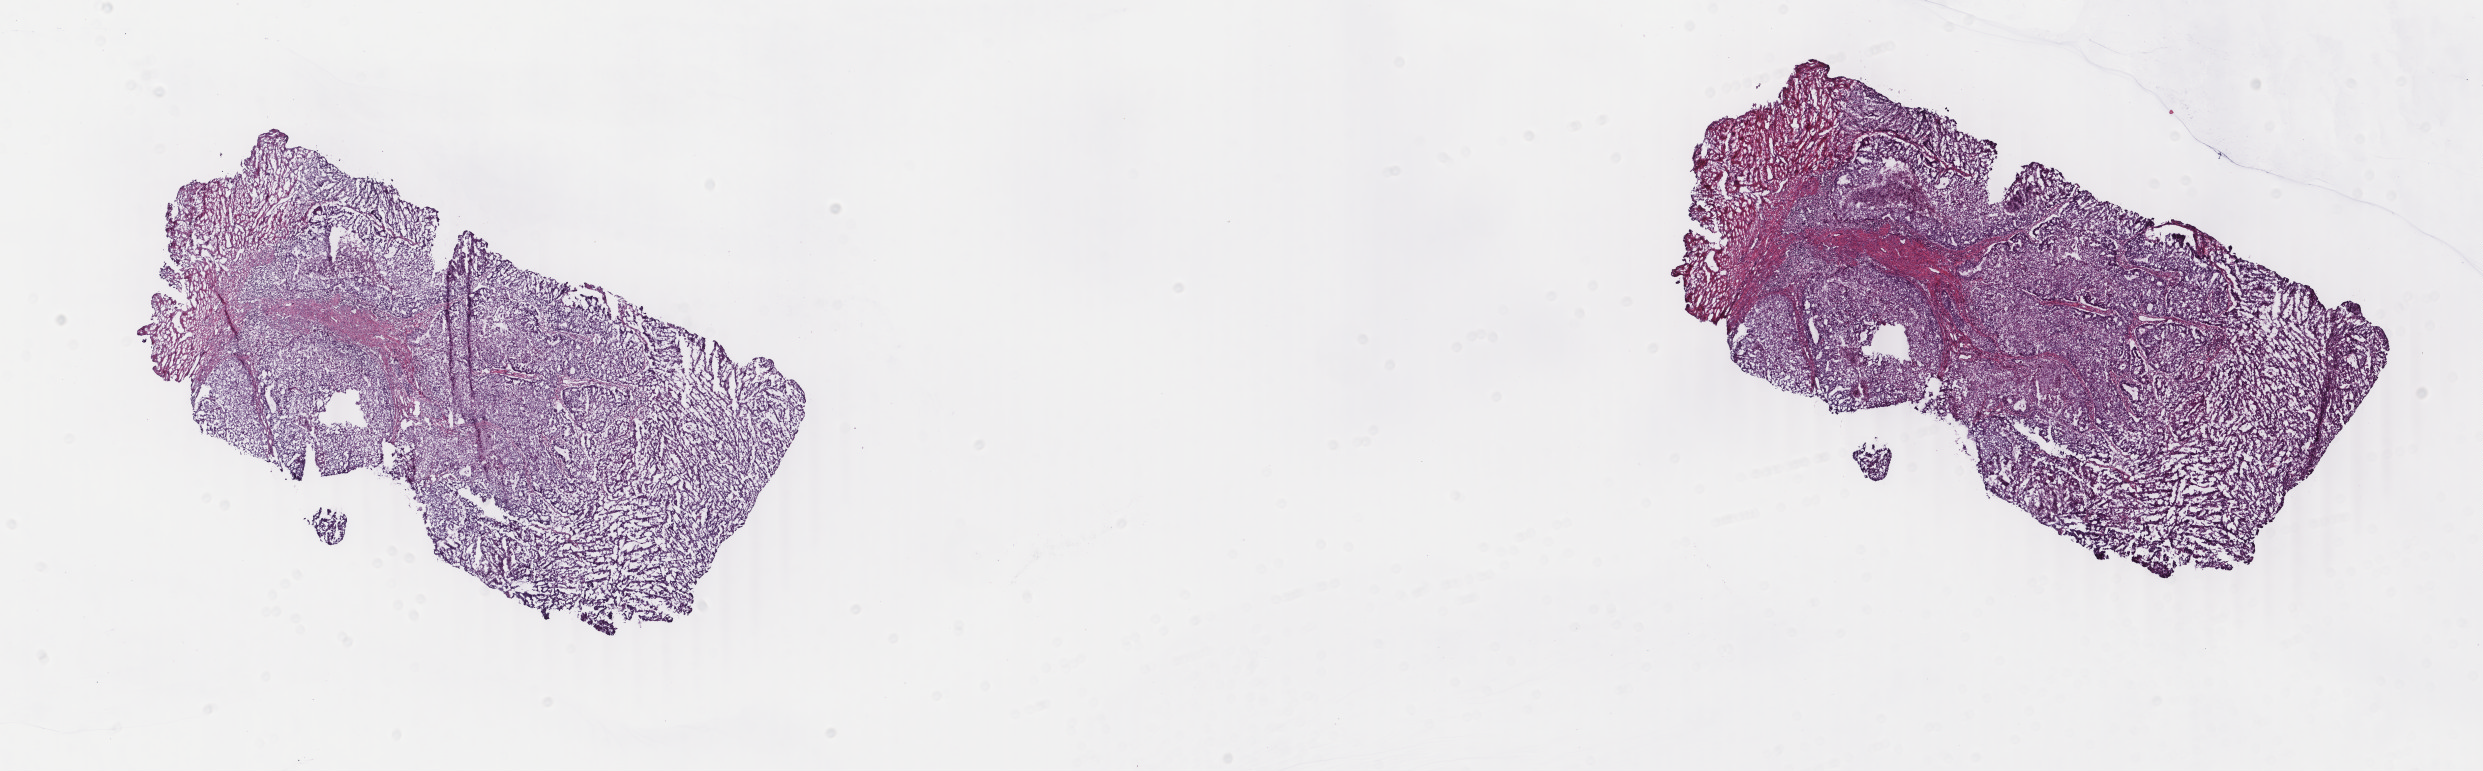
Whole-slide histology image, H&E-stained — low-resolution overview of the scanned area, about 19.8 x 6.1 mm; frozen section from the top of the tissue portion; uterus, primary tumour sample. Female patient; age at initial diagnosis 58 years. Histologic grade: G3 (poorly differentiated). Slide review estimates, as recorded: tumour cells 70%, tumour nuclei 80%, normal cells 0%, stromal cells 20%, necrosis 10%. Inflammatory infiltration, as recorded: lymphocyte infiltration 5%, monocyte infiltration 5%, neutrophil infiltration 5%.
* FIGO stage: IB
* histologic diagnosis: Endometrioid adenocarcinoma, NOS (endometrium)